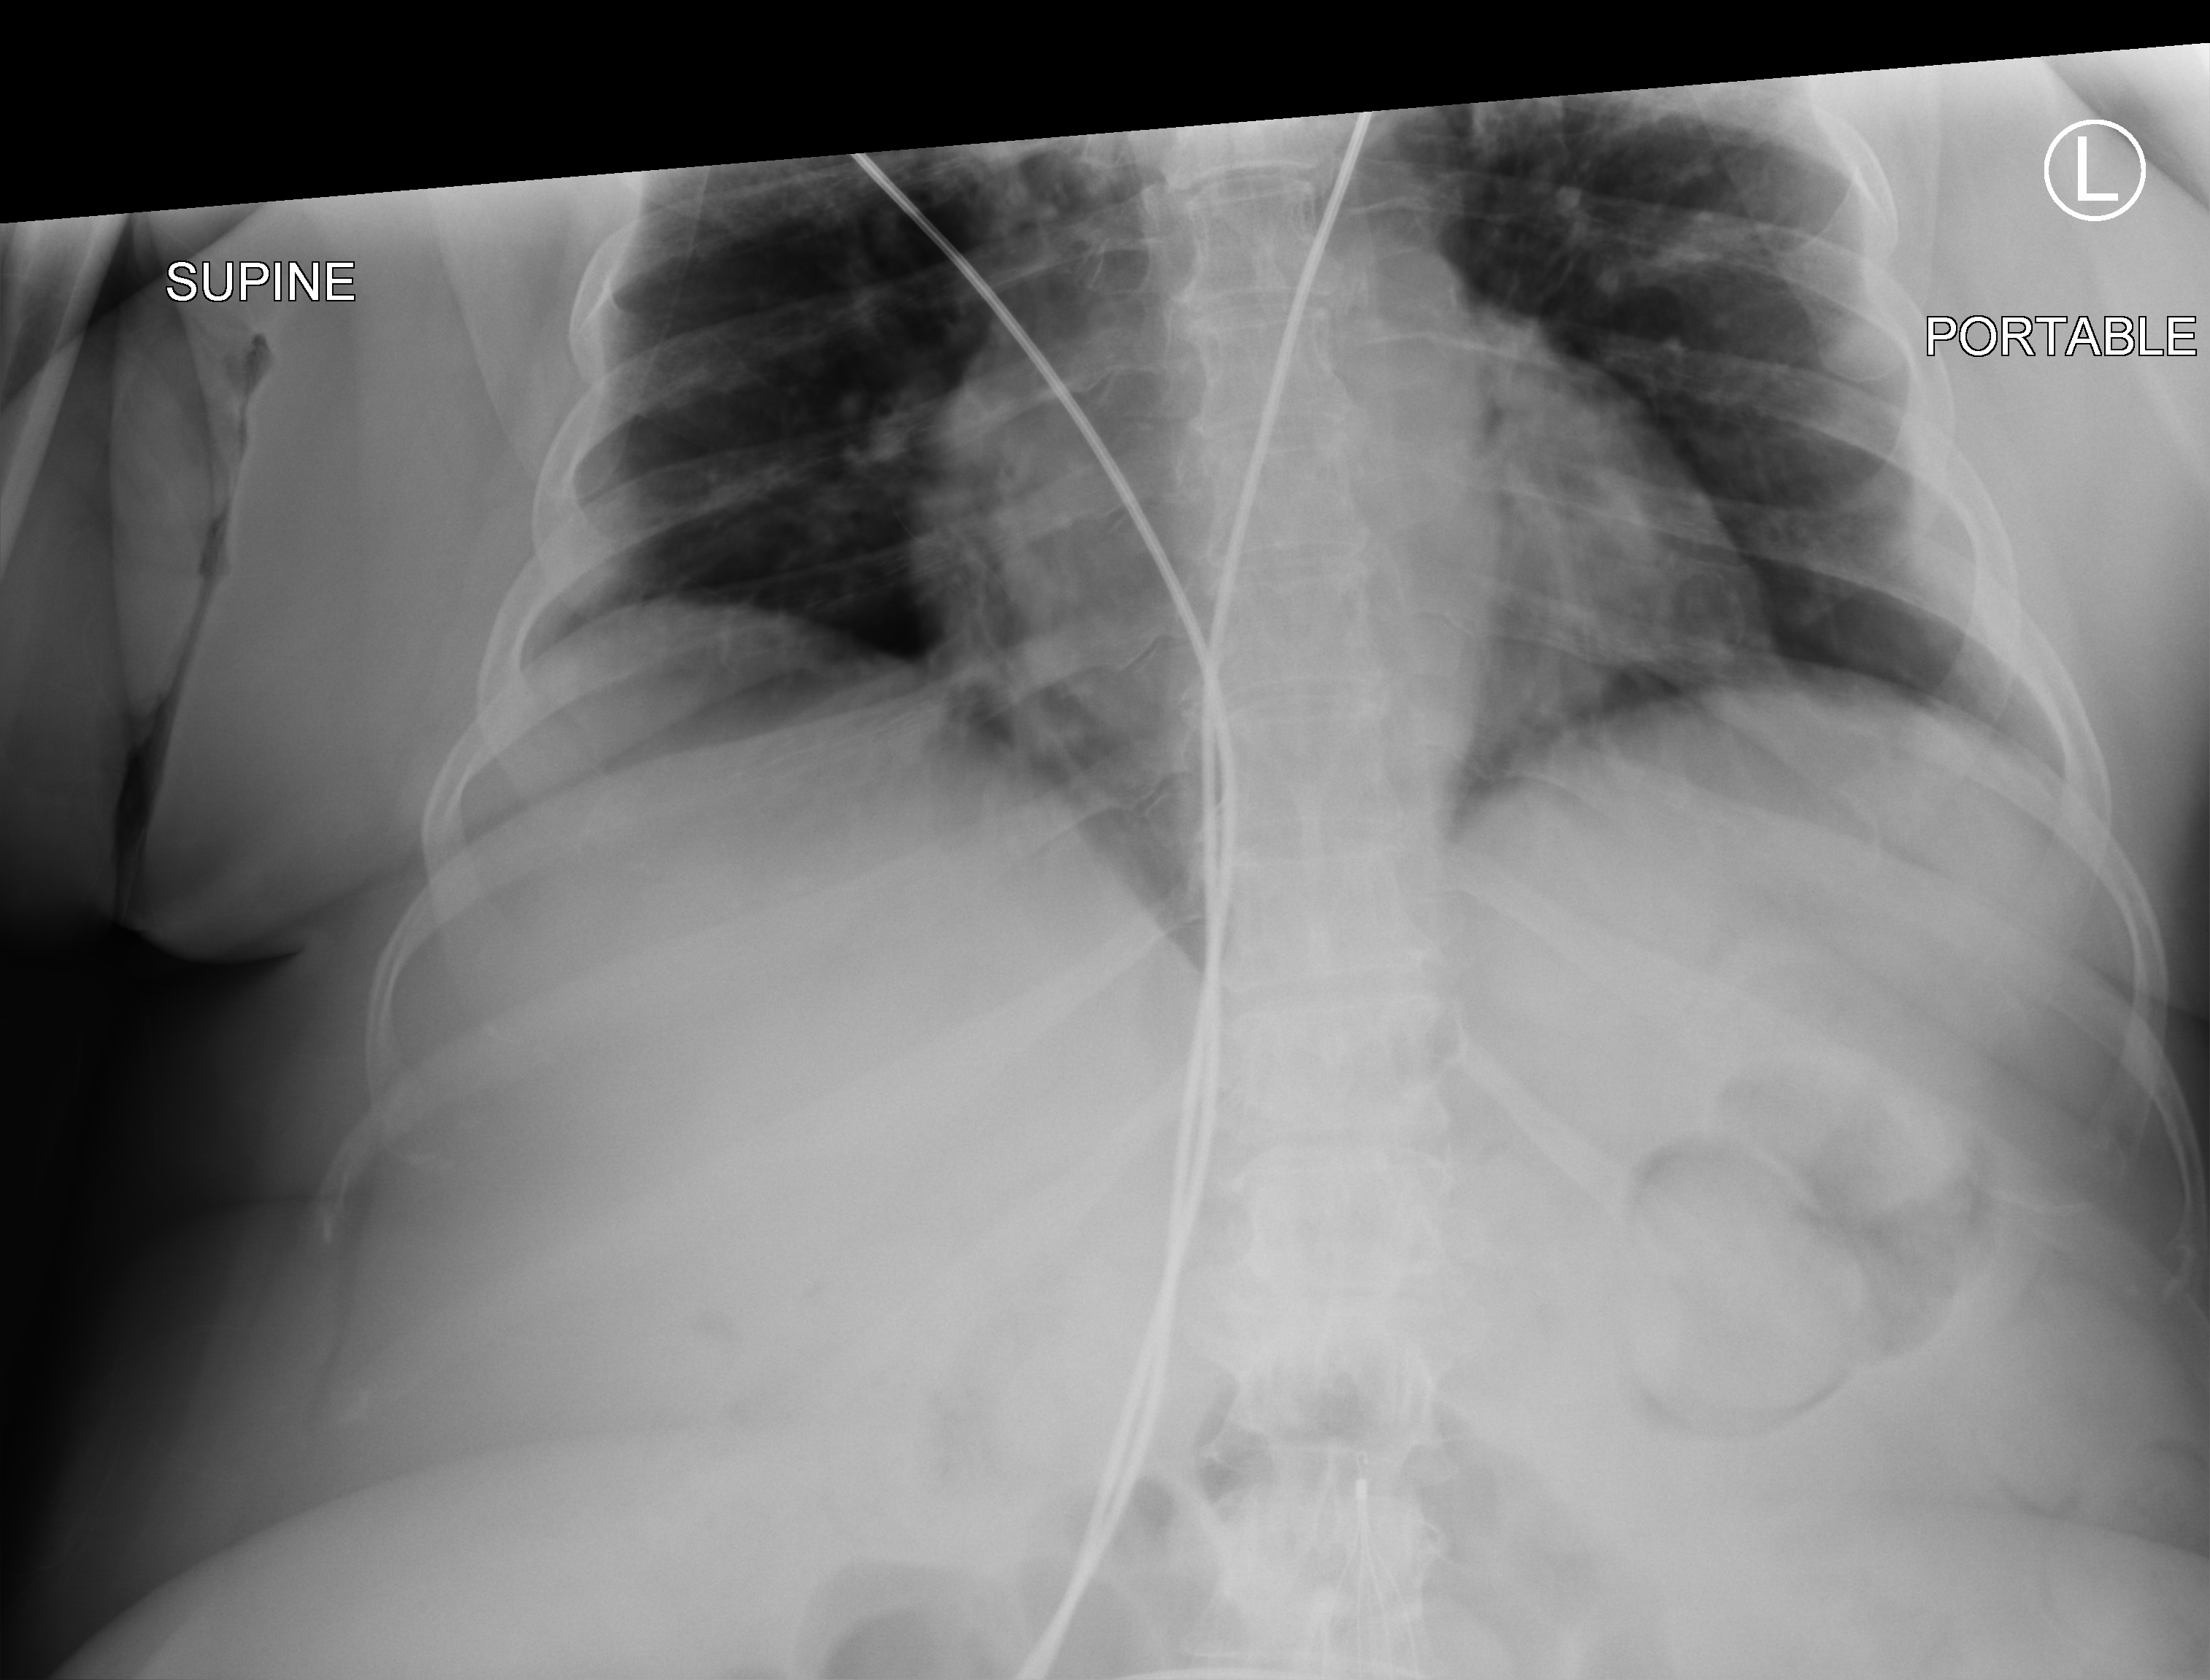
Portable abdomen radiograph. Female patient hospitalised with COVID-19, age 60–74 years.
Hospital-stay facts (about this admission, not read from this image; timing relative to this image not recorded):
- mechanically ventilated during this hospital stay: no
- admitted to intensive care during this hospital stay: no